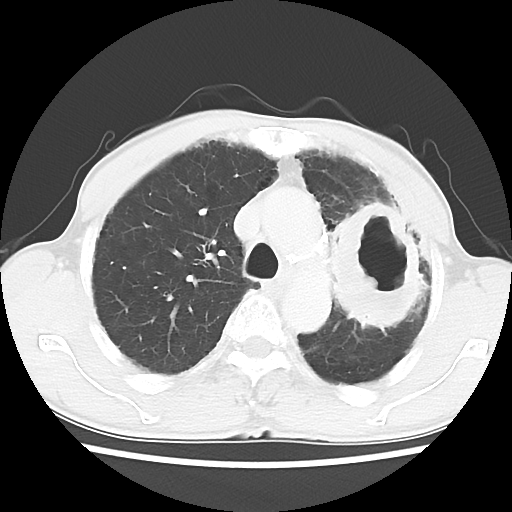
Chest CT, one axial slice; slice 43 of 60 in the series (ordered by position); lung window (W 1500 / L -600 HU); 512 × 512 image matrix, field of view 308 × 308 mm. Male patient, age 64 years. Case-level facts recorded for this patient, not image findings: clinical TNM (as recorded): T3 N3 M0; histopathological grade: G3.
Structures marked on this image (bounding box drawn by a radiologist):
- lung tumour (recorded histology: adenocarcinoma): bounding box (x1, y1, x2, y2) in pixels: (310, 194, 426, 338)